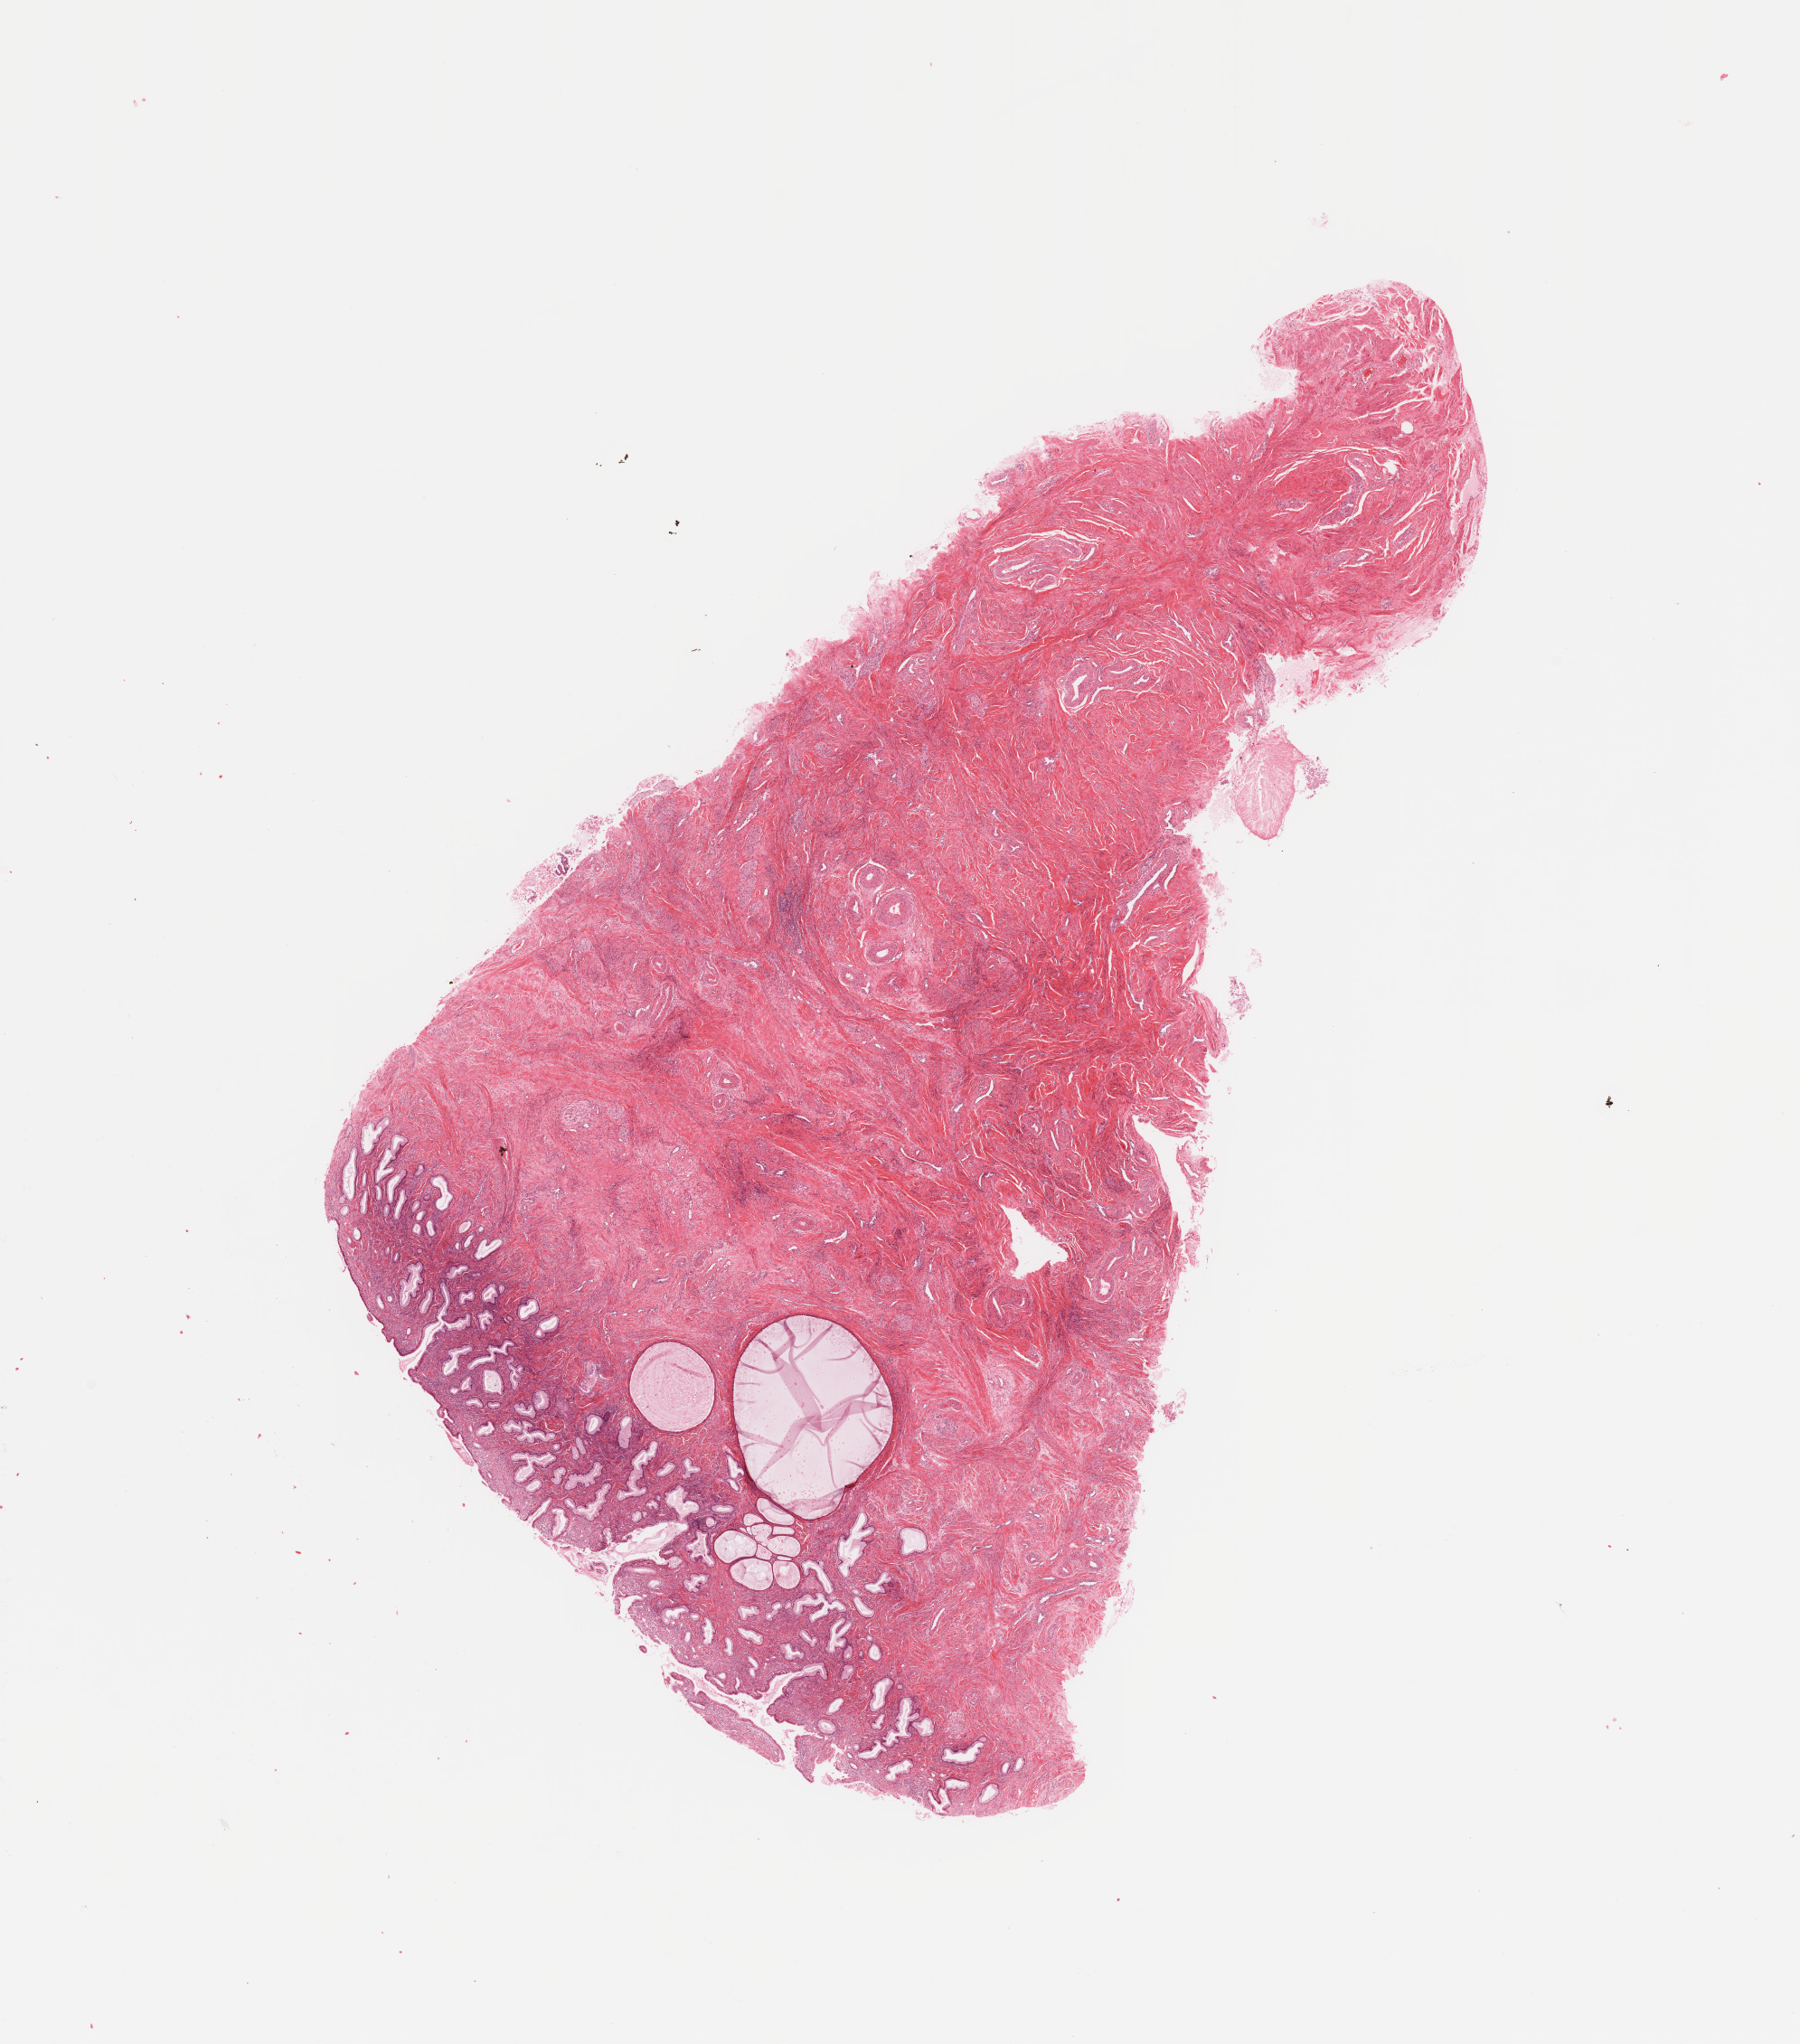
Digitized Hematoxylin and eosin (H&E) stained tissue section (whole slide), shown as a low-resolution overview of the whole scanned area (about 15.8 x 17.9 mm, slide scanned at 20x), normal (non-tumour) tissue sample, uterus. Patient: female, age 60 years.
This section: normal (non-tumour) tissue from the same patient. Patient diagnosis: Endometrioid adenocarcinoma, NOS.